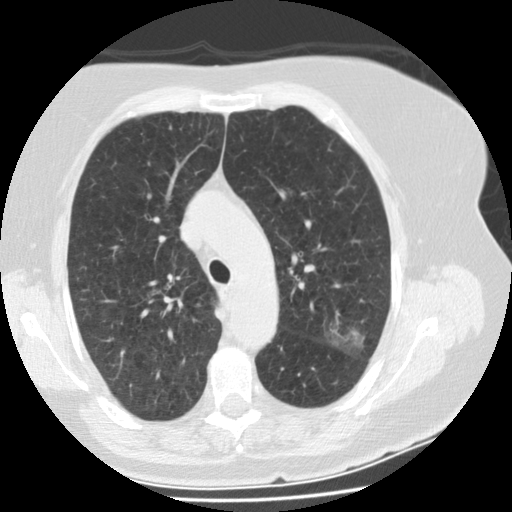
Low-dose screening chest CT, one axial slice. Position 110 of 151 along the scan axis. Reconstruction kernel STANDARD. 120 kVp. One of 2 acquisitions stored at this slice position. Lung window (W 1500 / L -600 HU). 2.5 mm slice thickness. 512 × 512 image matrix.
Structures marked on this image (expert manual segmentation):
- lesion 1 (tumor, upper lobe of left lung): bounding box <327,322,366,356> (left, top, right, bottom; pixels)